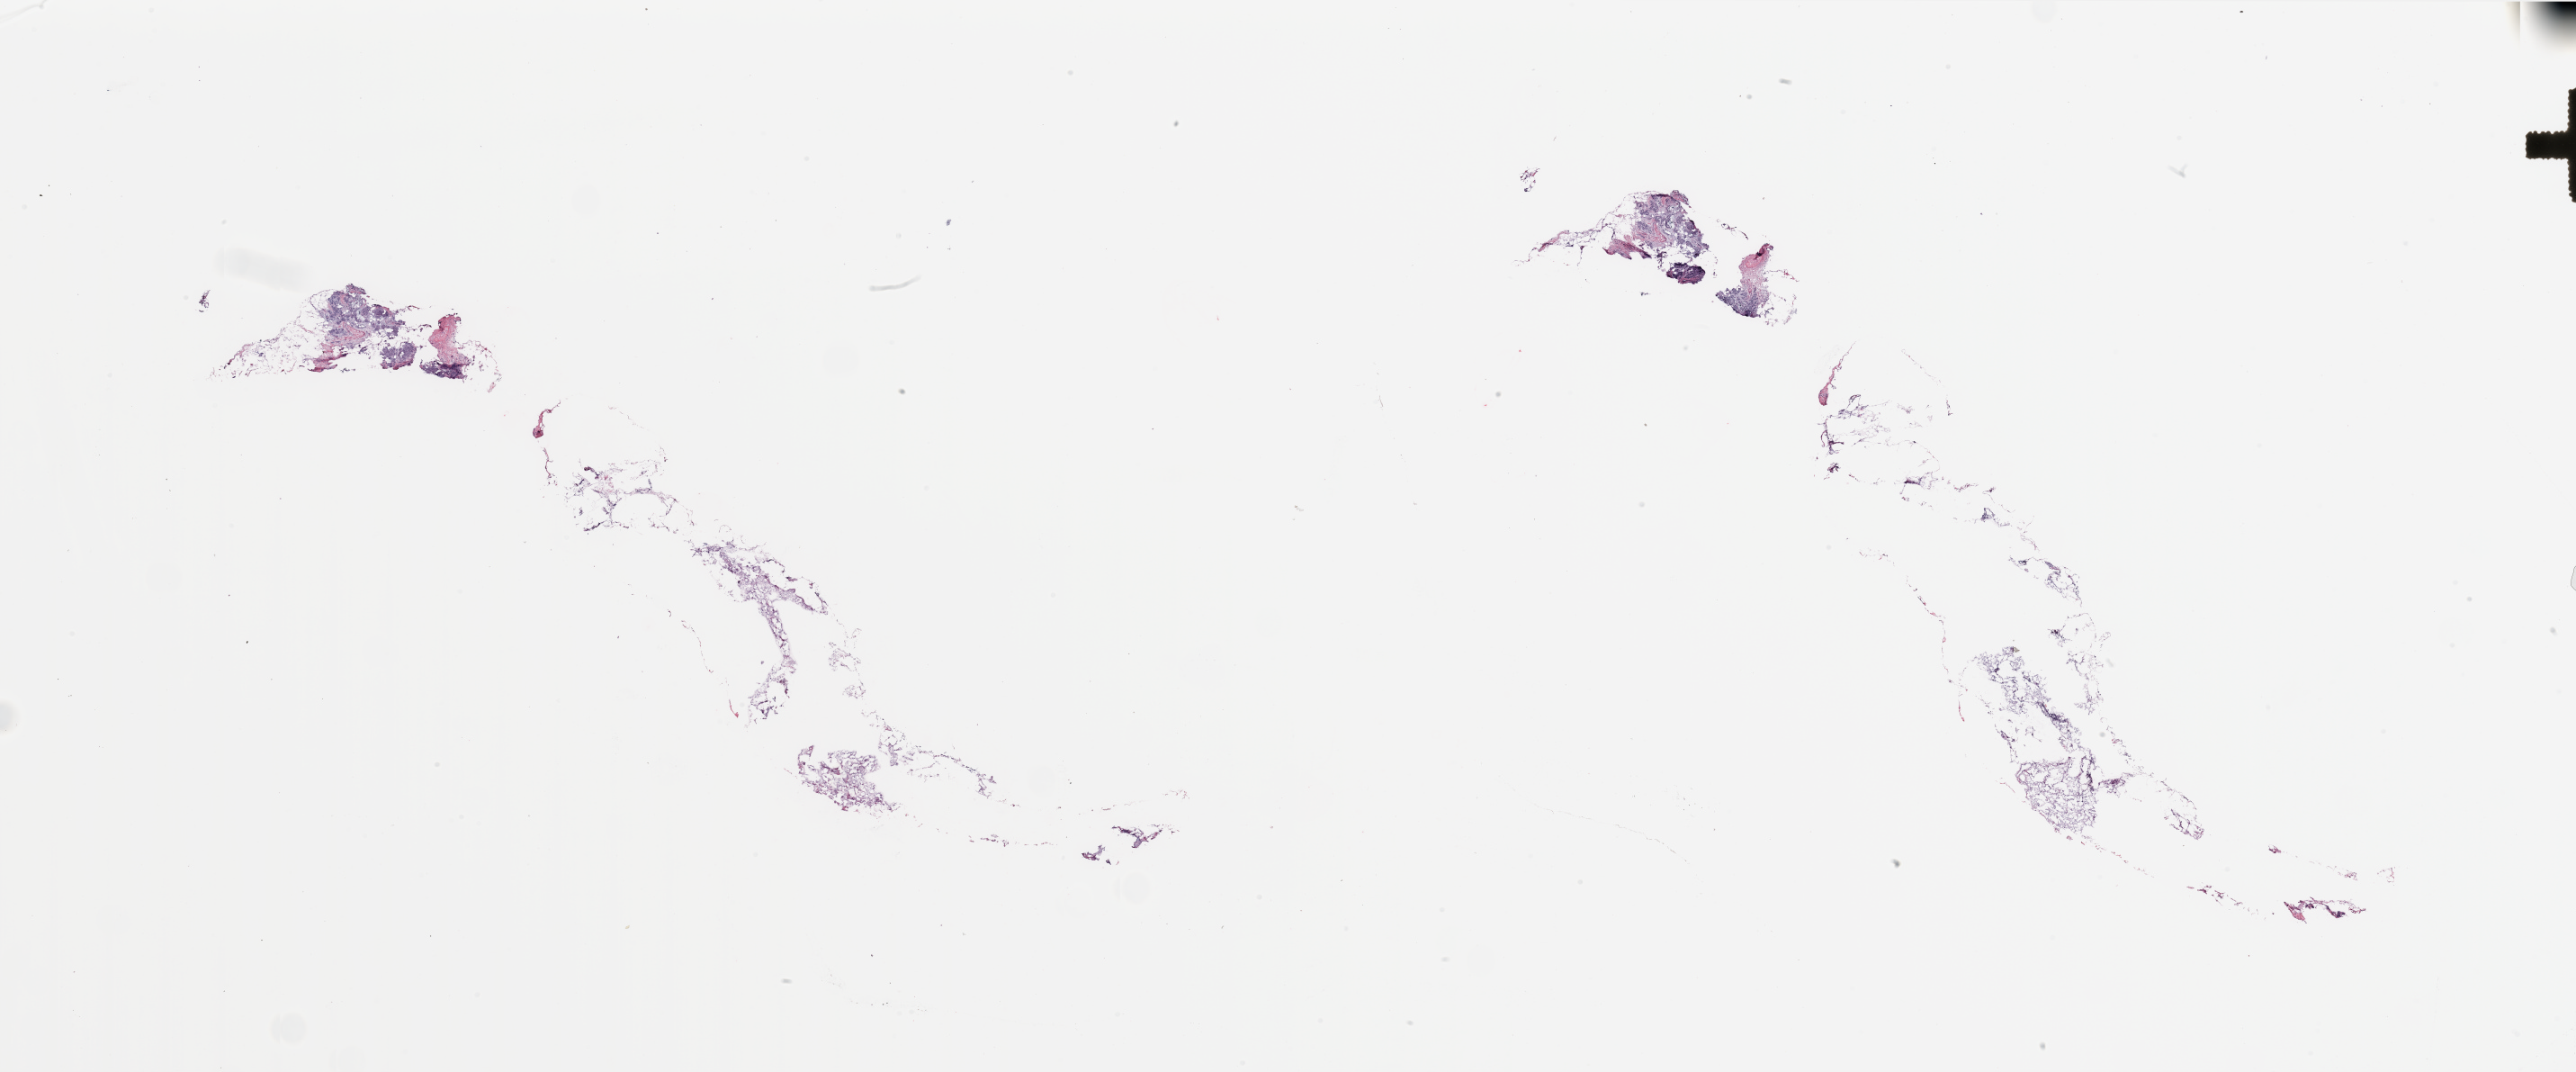
Whole-slide histology image, Hematoxylin and eosin (H&E) stained — shown as a low-resolution overview of the whole scanned area (about 45.3 x 18.8 mm), breast, tissue type not recorded.
- patient diagnosis (cohort enrolment): breast cancer (breast)